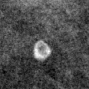
Crop from a digitized film mammogram around one marked abnormality; right breast; CC view.
Finding: calcifications, morphology lucent center; BI-RADS assessment category 2; subtlety rating 3 on a 1 (subtle) to 5 (obvious) scale; benign; no additional work-up was recommended (benign without callback).